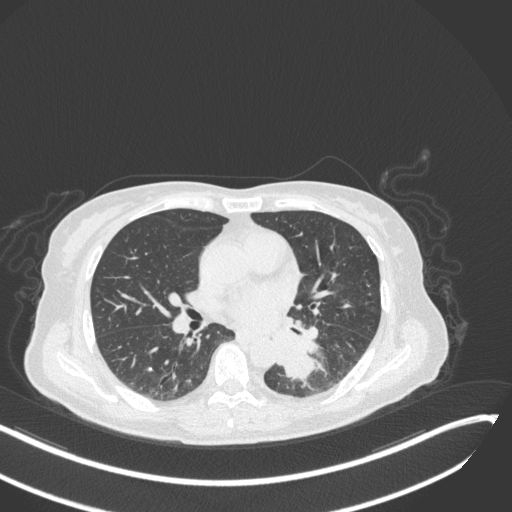
Chest CT, one axial slice; slice 137 of 342 in the series (ordered by position); reconstruction kernel B31f; lung window (W 1500 / L -600 HU); 1 mm slice thickness; 512 × 512 image matrix, field of view 400 × 400 mm. Patient: female, 64 years. Case-level facts recorded for this patient, not image findings: clinical TNM (as recorded): T3 N1 M1.
Structures marked on this image (rectangle marked by the reading radiologist):
- lung tumour (recorded histology: small cell carcinoma): bounding box (x1, y1, x2, y2) in pixels: (268, 340, 324, 393)